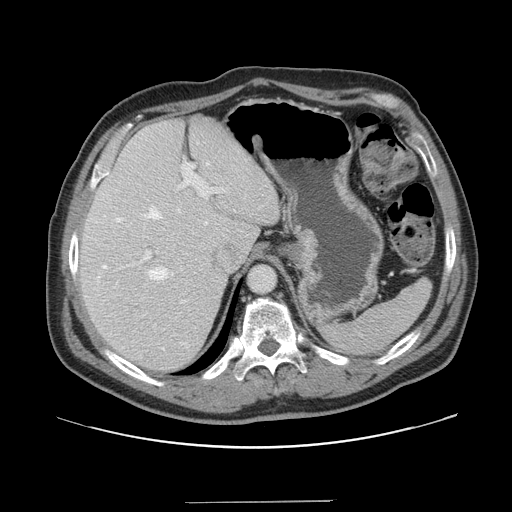
Contrast-enhanced abdominal CT, one axial slice; slice 112 of 151 in the series (ordered by position); 120 kVp; intravenous contrast given; soft-tissue window (W 400 / L 40 HU); 512 × 512 image matrix, field of view 399 × 399 mm. Male patient, age 63 years. Case-level facts recorded for this patient, not image findings: diagnosis: colorectal cancer liver metastases, imaged before liver resection; multiple liver metastases: no; largest metastasis: 2.1 cm; disease in both lobes: no.
Structures marked on this image (outlined manually by an expert reader):
- hepatic veins: bounding box <103,162,209,280> (left, top, right, bottom; pixels)
- liver: <78,117,279,373>
- planned liver remnant (the part of the liver to remain after resection): <79,118,267,373>
- portal vein (with intrahepatic branches): <141,162,226,303>